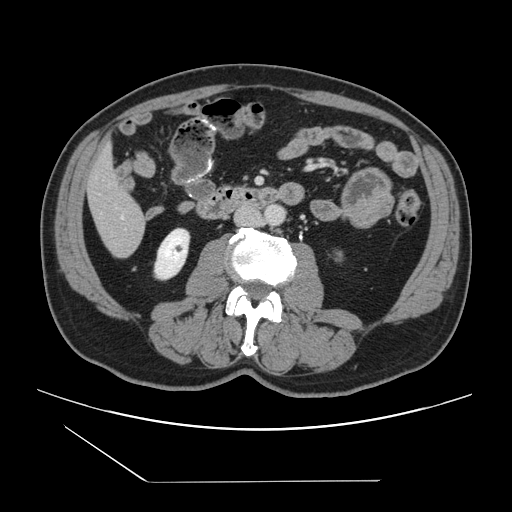
Contrast-enhanced abdominal CT, one axial slice. Position 29 of 157 along the scan axis. Soft-tissue window (W 400 / L 40 HU). 512 × 512 image matrix, field of view 407 × 407 mm. Male patient, age 61 years. Case-level facts recorded for this patient, not image findings: diagnosis: colorectal cancer liver metastases, imaged before liver resection; multiple liver metastases: yes; largest metastasis: 5.5 cm; disease in both lobes: yes.
Outlined on this slice (manually delineated by an expert):
- hepatic veins: bounding box (x1, y1, x2, y2) in pixels: (121, 216, 124, 218)
- liver: (89, 151, 146, 257)
- planned liver remnant (the part of the liver to remain after resection): (88, 151, 141, 219)